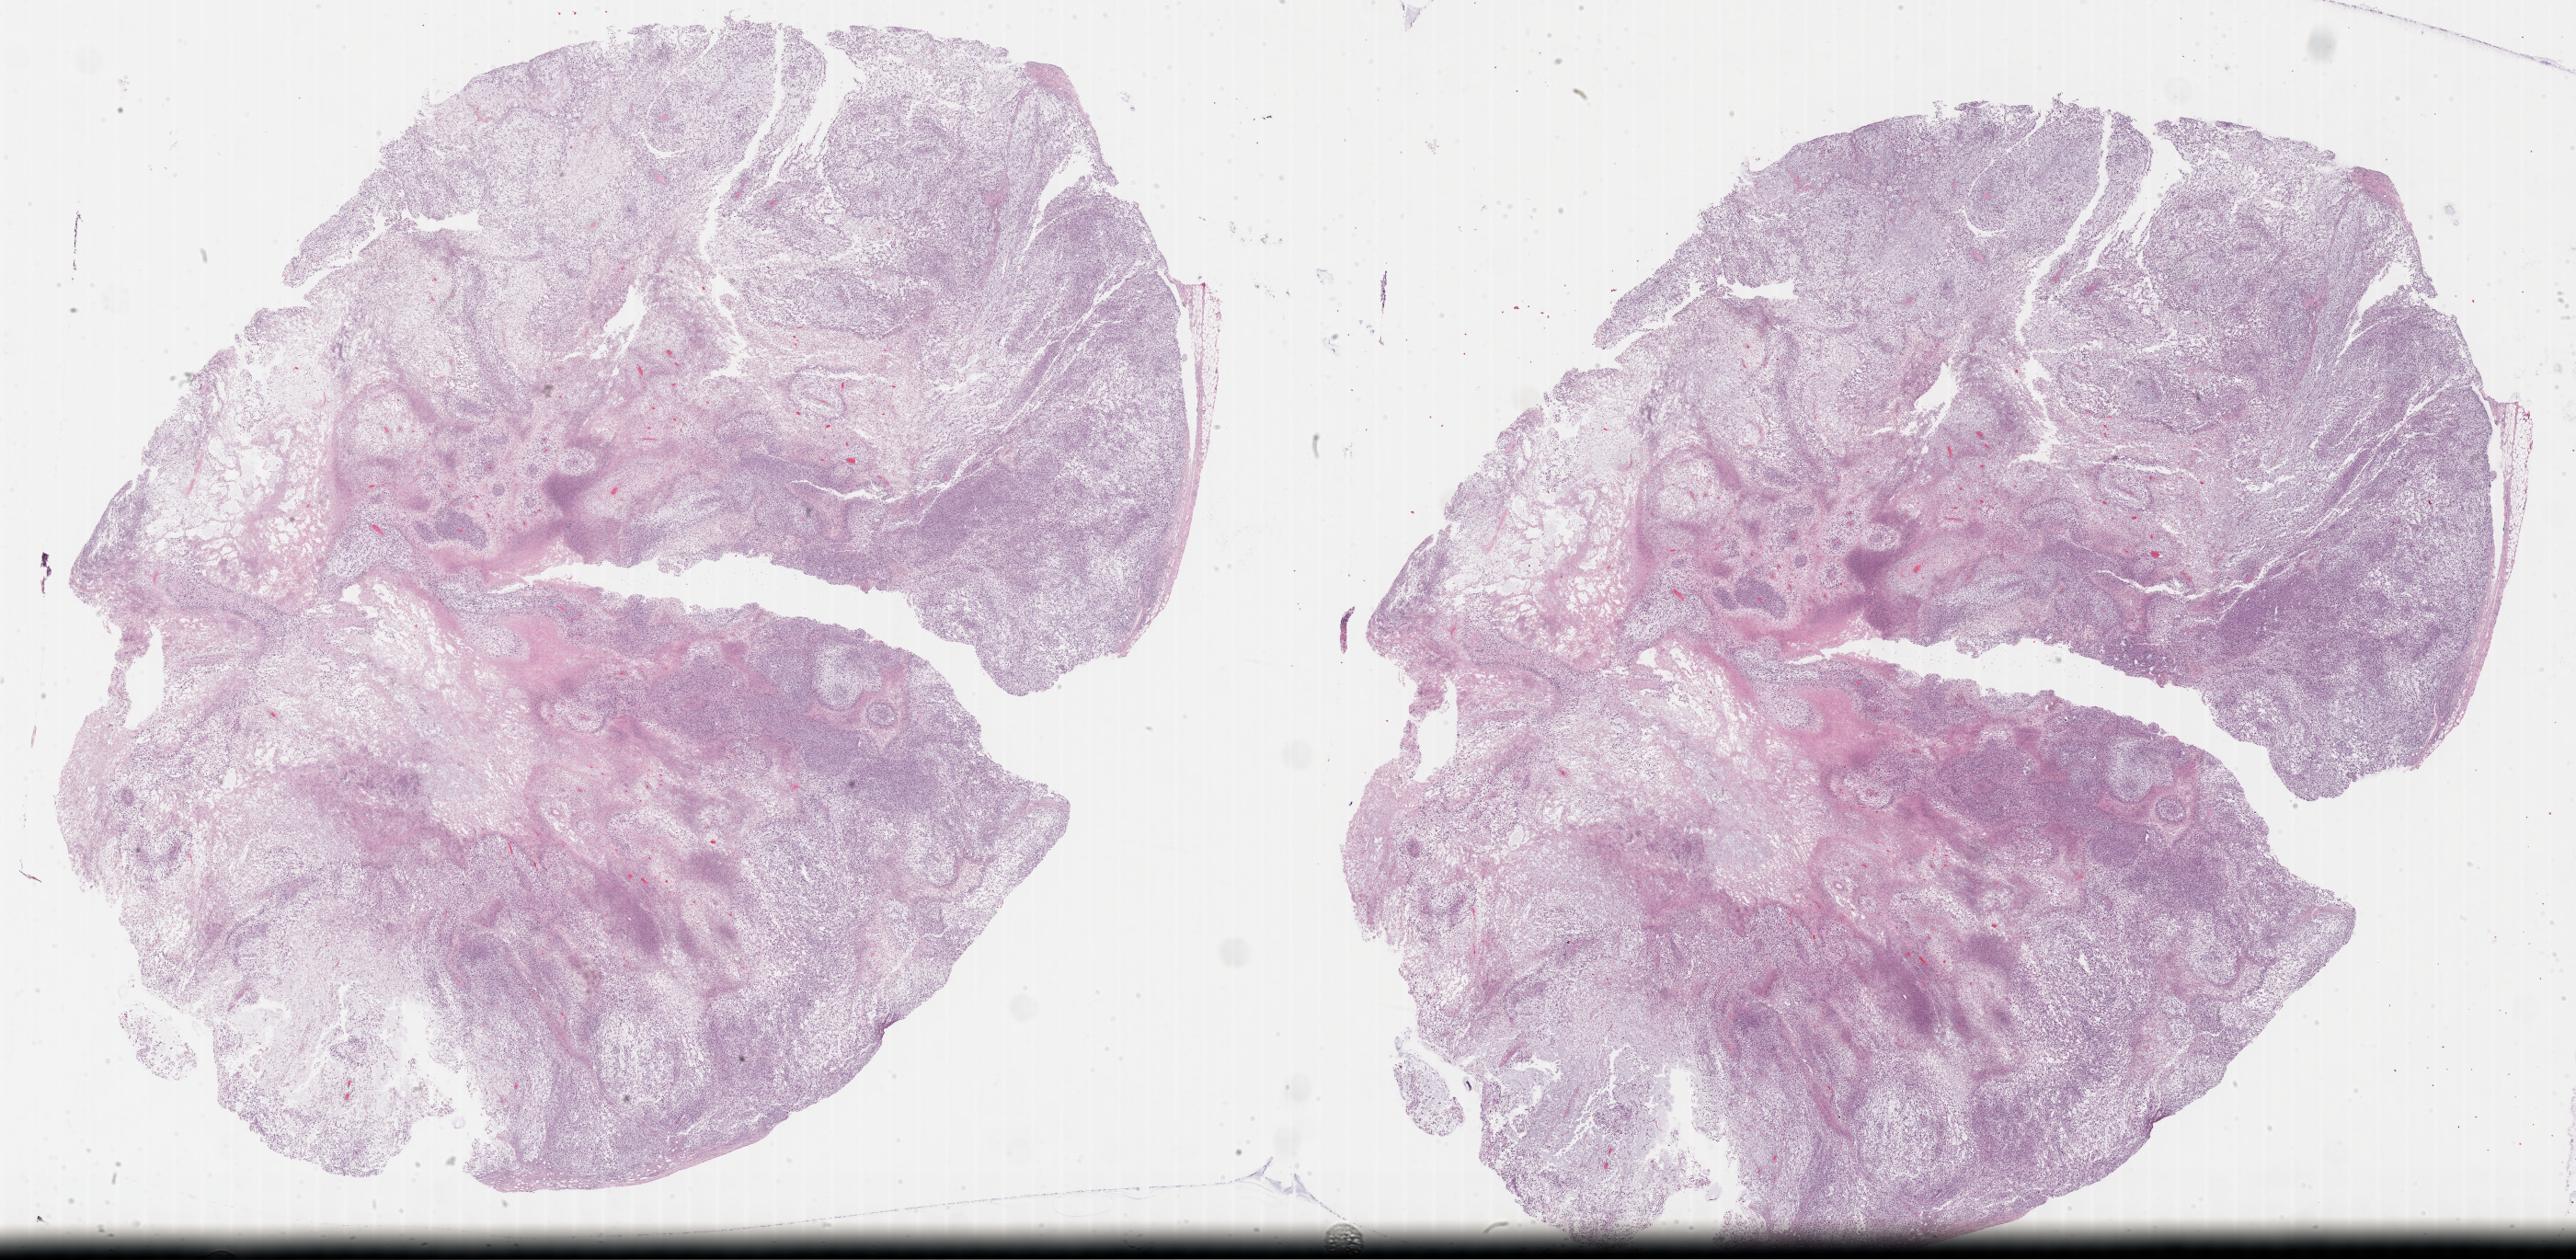
Digitized Hematoxylin and eosin (H&E) stained tissue section (whole slide) — a low-resolution overview of the entire scanned area, about 45.3 x 22.2 mm (slide scanned at 40x), formalin-fixed paraffin-embedded (FFPE) diagnostic section, sample: primary tumour, connective, subcutaneous and other soft tissues. Male, age 60 years at initial diagnosis.
Pathologic diagnosis: Fibromyxosarcoma (connective, subcutaneous and other soft tissues of thorax).